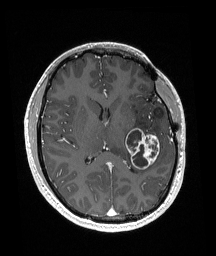
Brain MRI from a brain-tumour surgery series, one axial slice. Position 86 of 192 along the scan axis. T1-weighted post-contrast. 1 mm slice thickness. 216 × 256 image matrix, field of view 211 × 250 mm. From the clinical record (not read from this slice): histopathology: Glioneuronal tumor; WHO grade: 2; tumour location: Left Superior Temporal Gyrus.
Outlined on this slice (manually delineated by an expert):
- tumour: bounding box (x1, y1, x2, y2) in pixels: (126, 128, 160, 169)